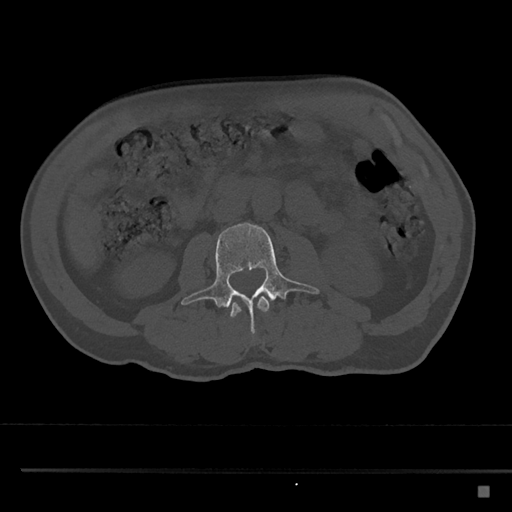
CT including the spine, one axial slice. Position 707 of 797 along the scan axis. Reconstruction kernel Br40s/3. Bone window (W 1800 / L 400 HU). 0.5 mm slice thickness. 512 × 512 image matrix, field of view 391 × 391 mm. Male patient, age 59 years. Case-level facts recorded for this patient, not image findings: primary cancer: prostate.
Structures marked on this image (semi-automatically segmented with operator editing):
- L2 vertebra: bounding box <228,296,270,318> (left, top, right, bottom; pixels)
- L3 vertebra: <181,222,319,336>